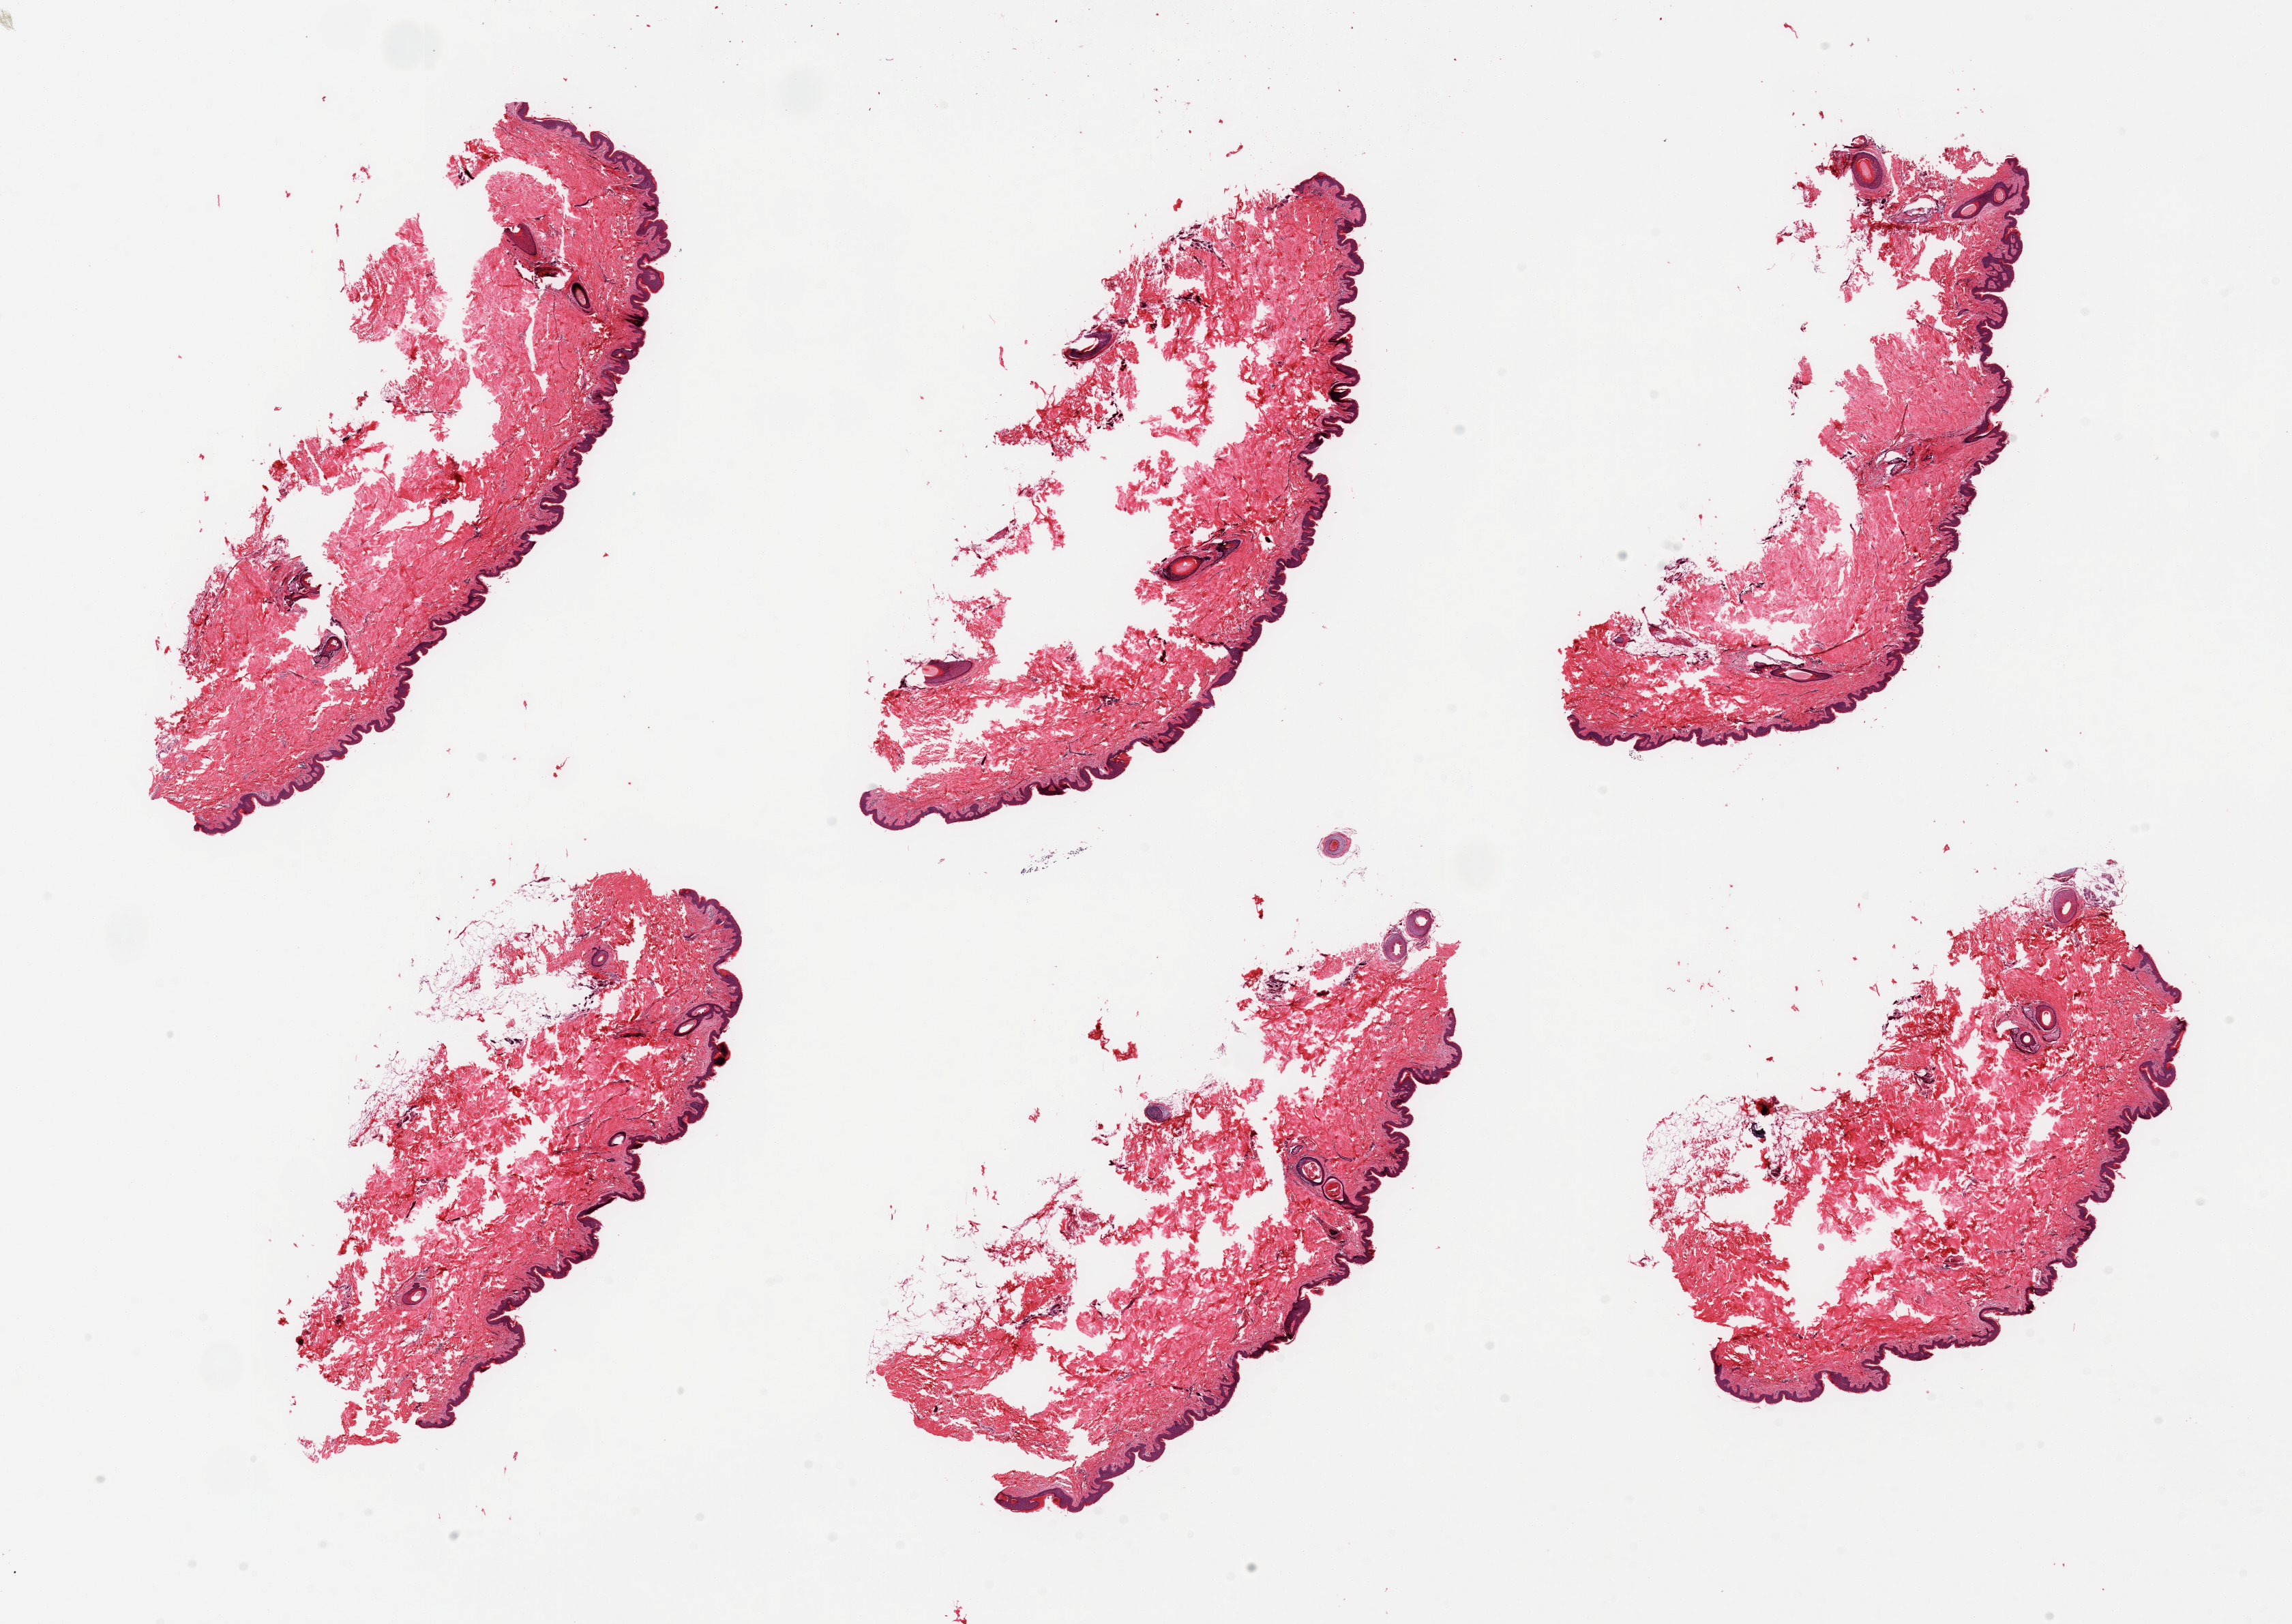
Digitized haematoxylin and eosin-stained section, low-resolution overview of the scanned area, about 26.6 x 18.8 mm; PAXgene-fixed, paraffin-embedded tissue; sampled site (target tissue): skin of suprapubic region; tissue donor sample. Donor sex: male.
Reviewer comment on this tissue sample: 6 pieces; largely disrupted sections, some residual fat.